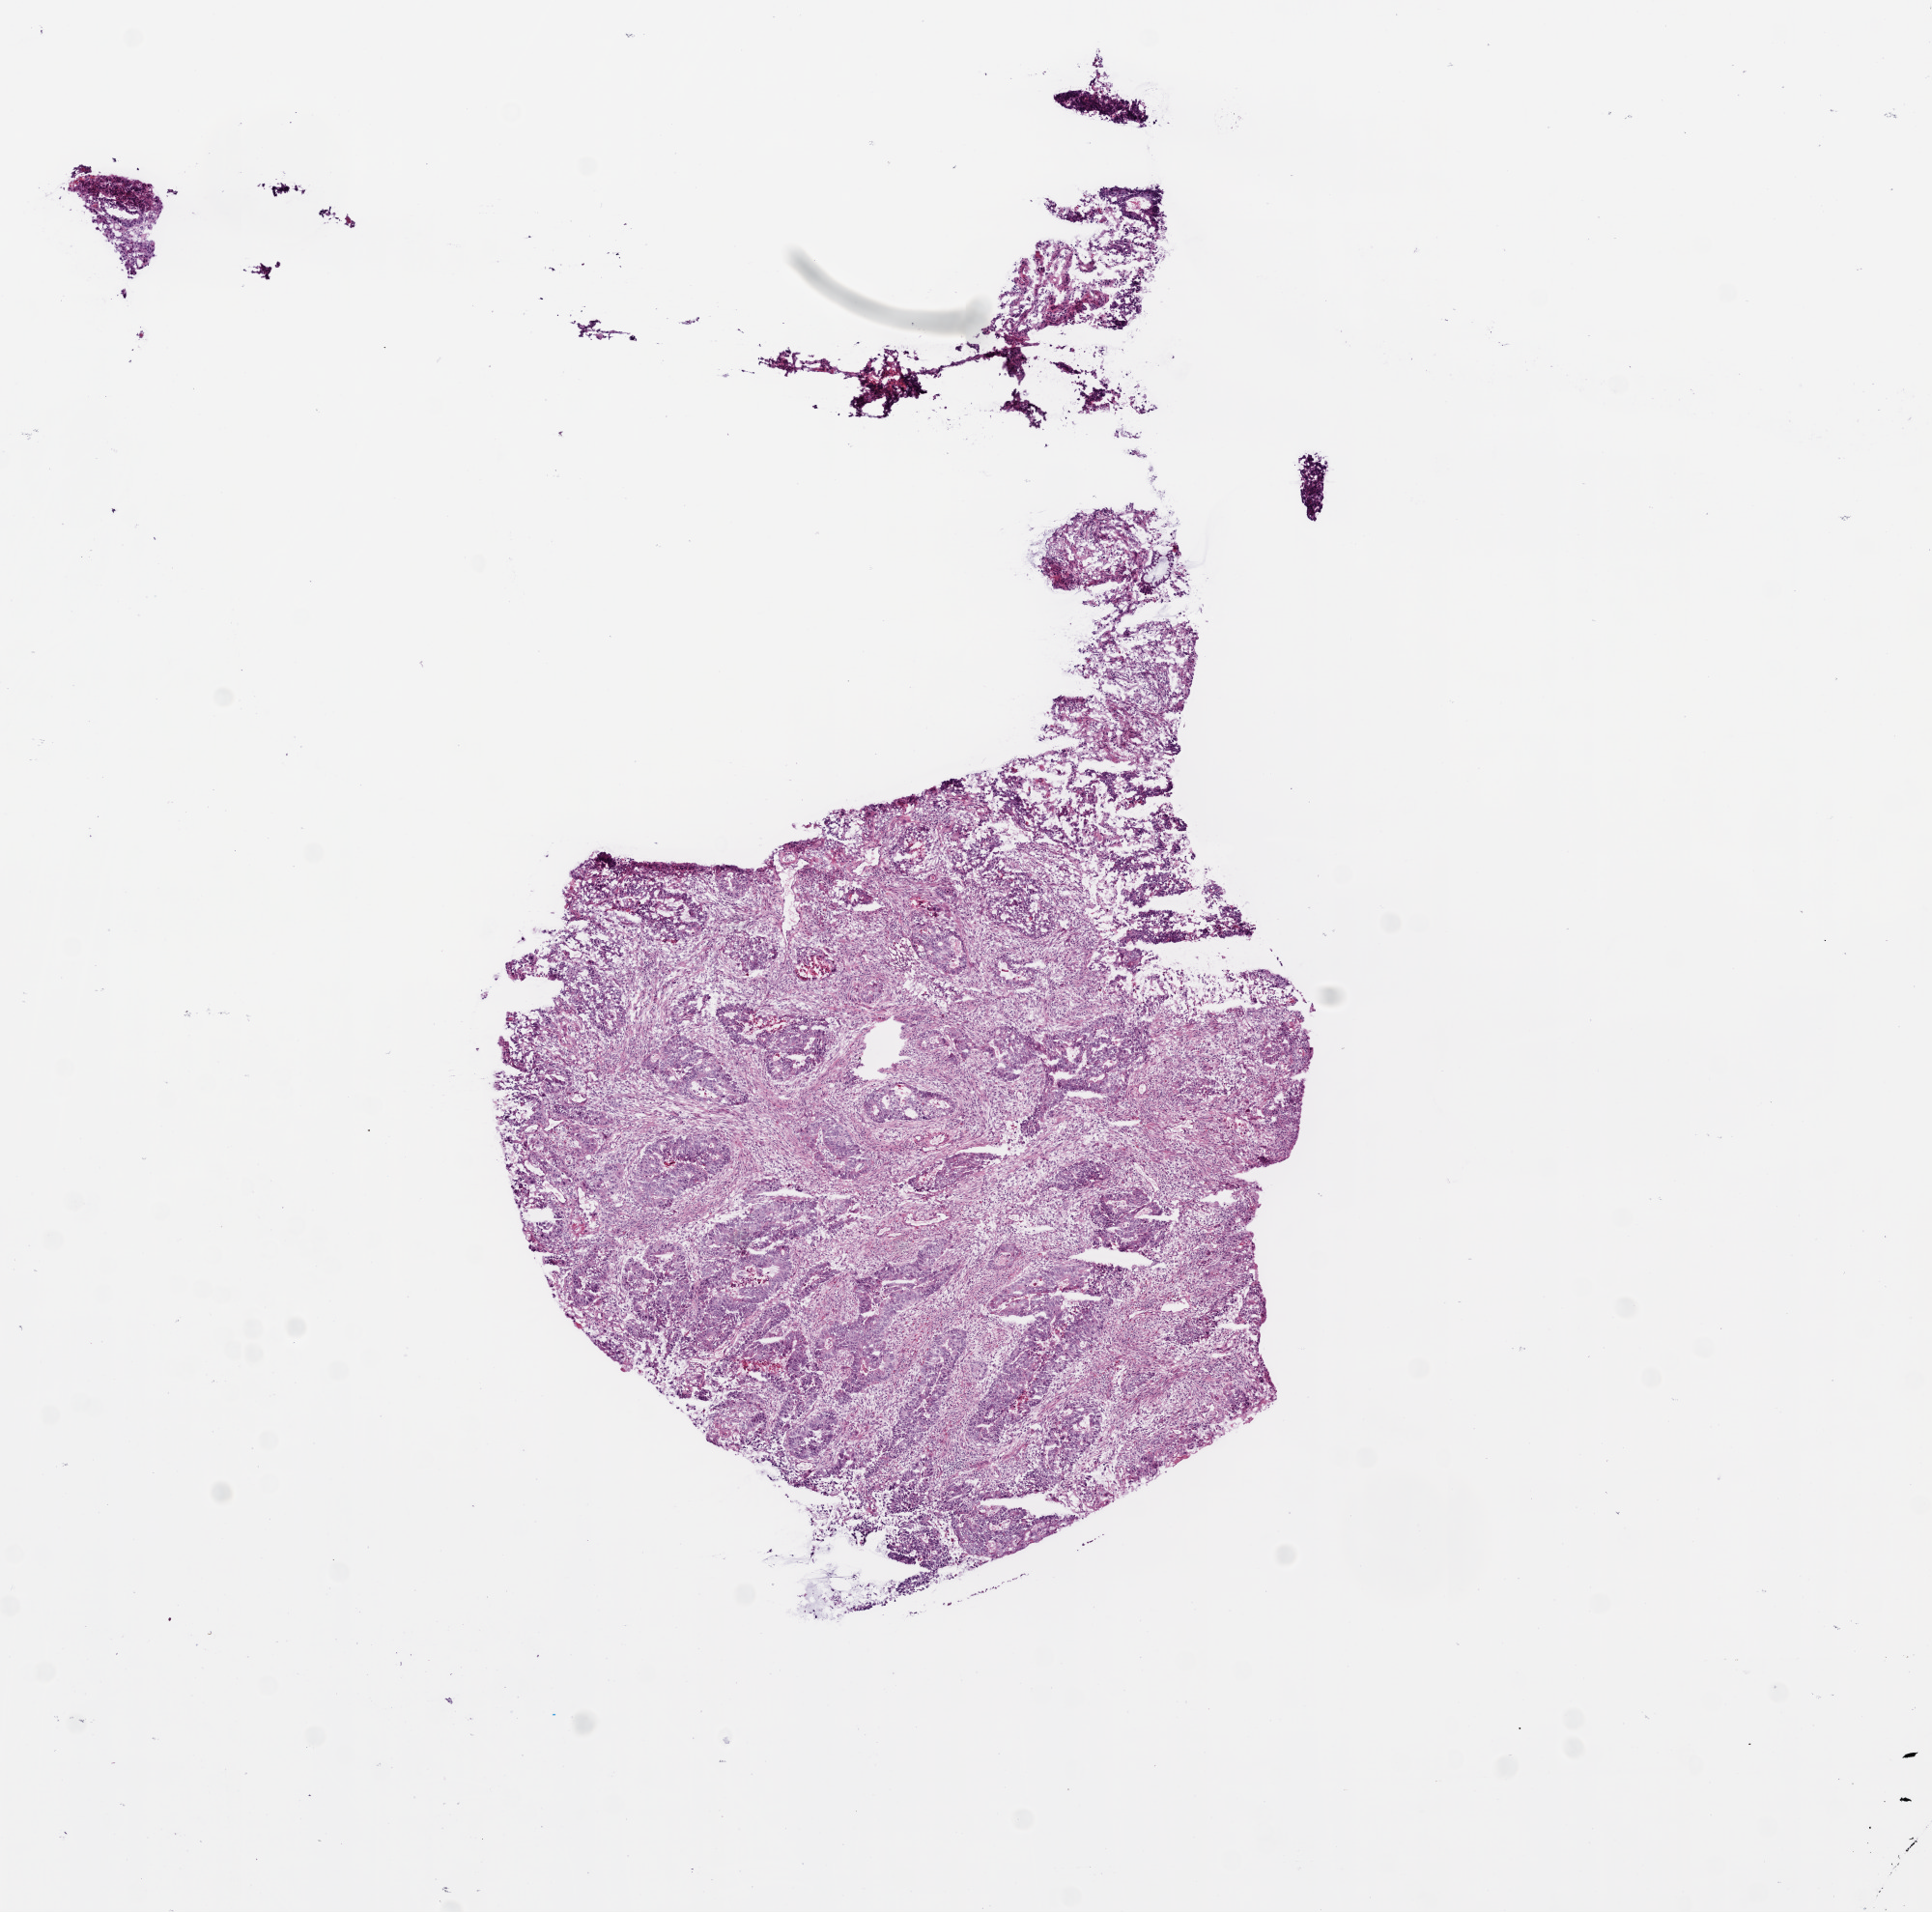
Hematoxylin and eosin (H&E) stained whole-slide image — a low-resolution overview of the entire scanned area, about 8.0 x 7.9 mm (acquisition: 20x scan); frozen section from the bottom of the tissue portion; rectum, primary tumour sample. Male, age 69 years at initial diagnosis. Composition of this section per pathologist review: tumour cells 45%, tumour nuclei 70%, normal cells 0%, stromal cells 40%, necrosis 15%.
AJCC pathologic stage: I (6th edition). Lymph nodes positive (case pathology): 0 of 15 examined. Pathologic diagnosis: Adenocarcinoma, NOS.